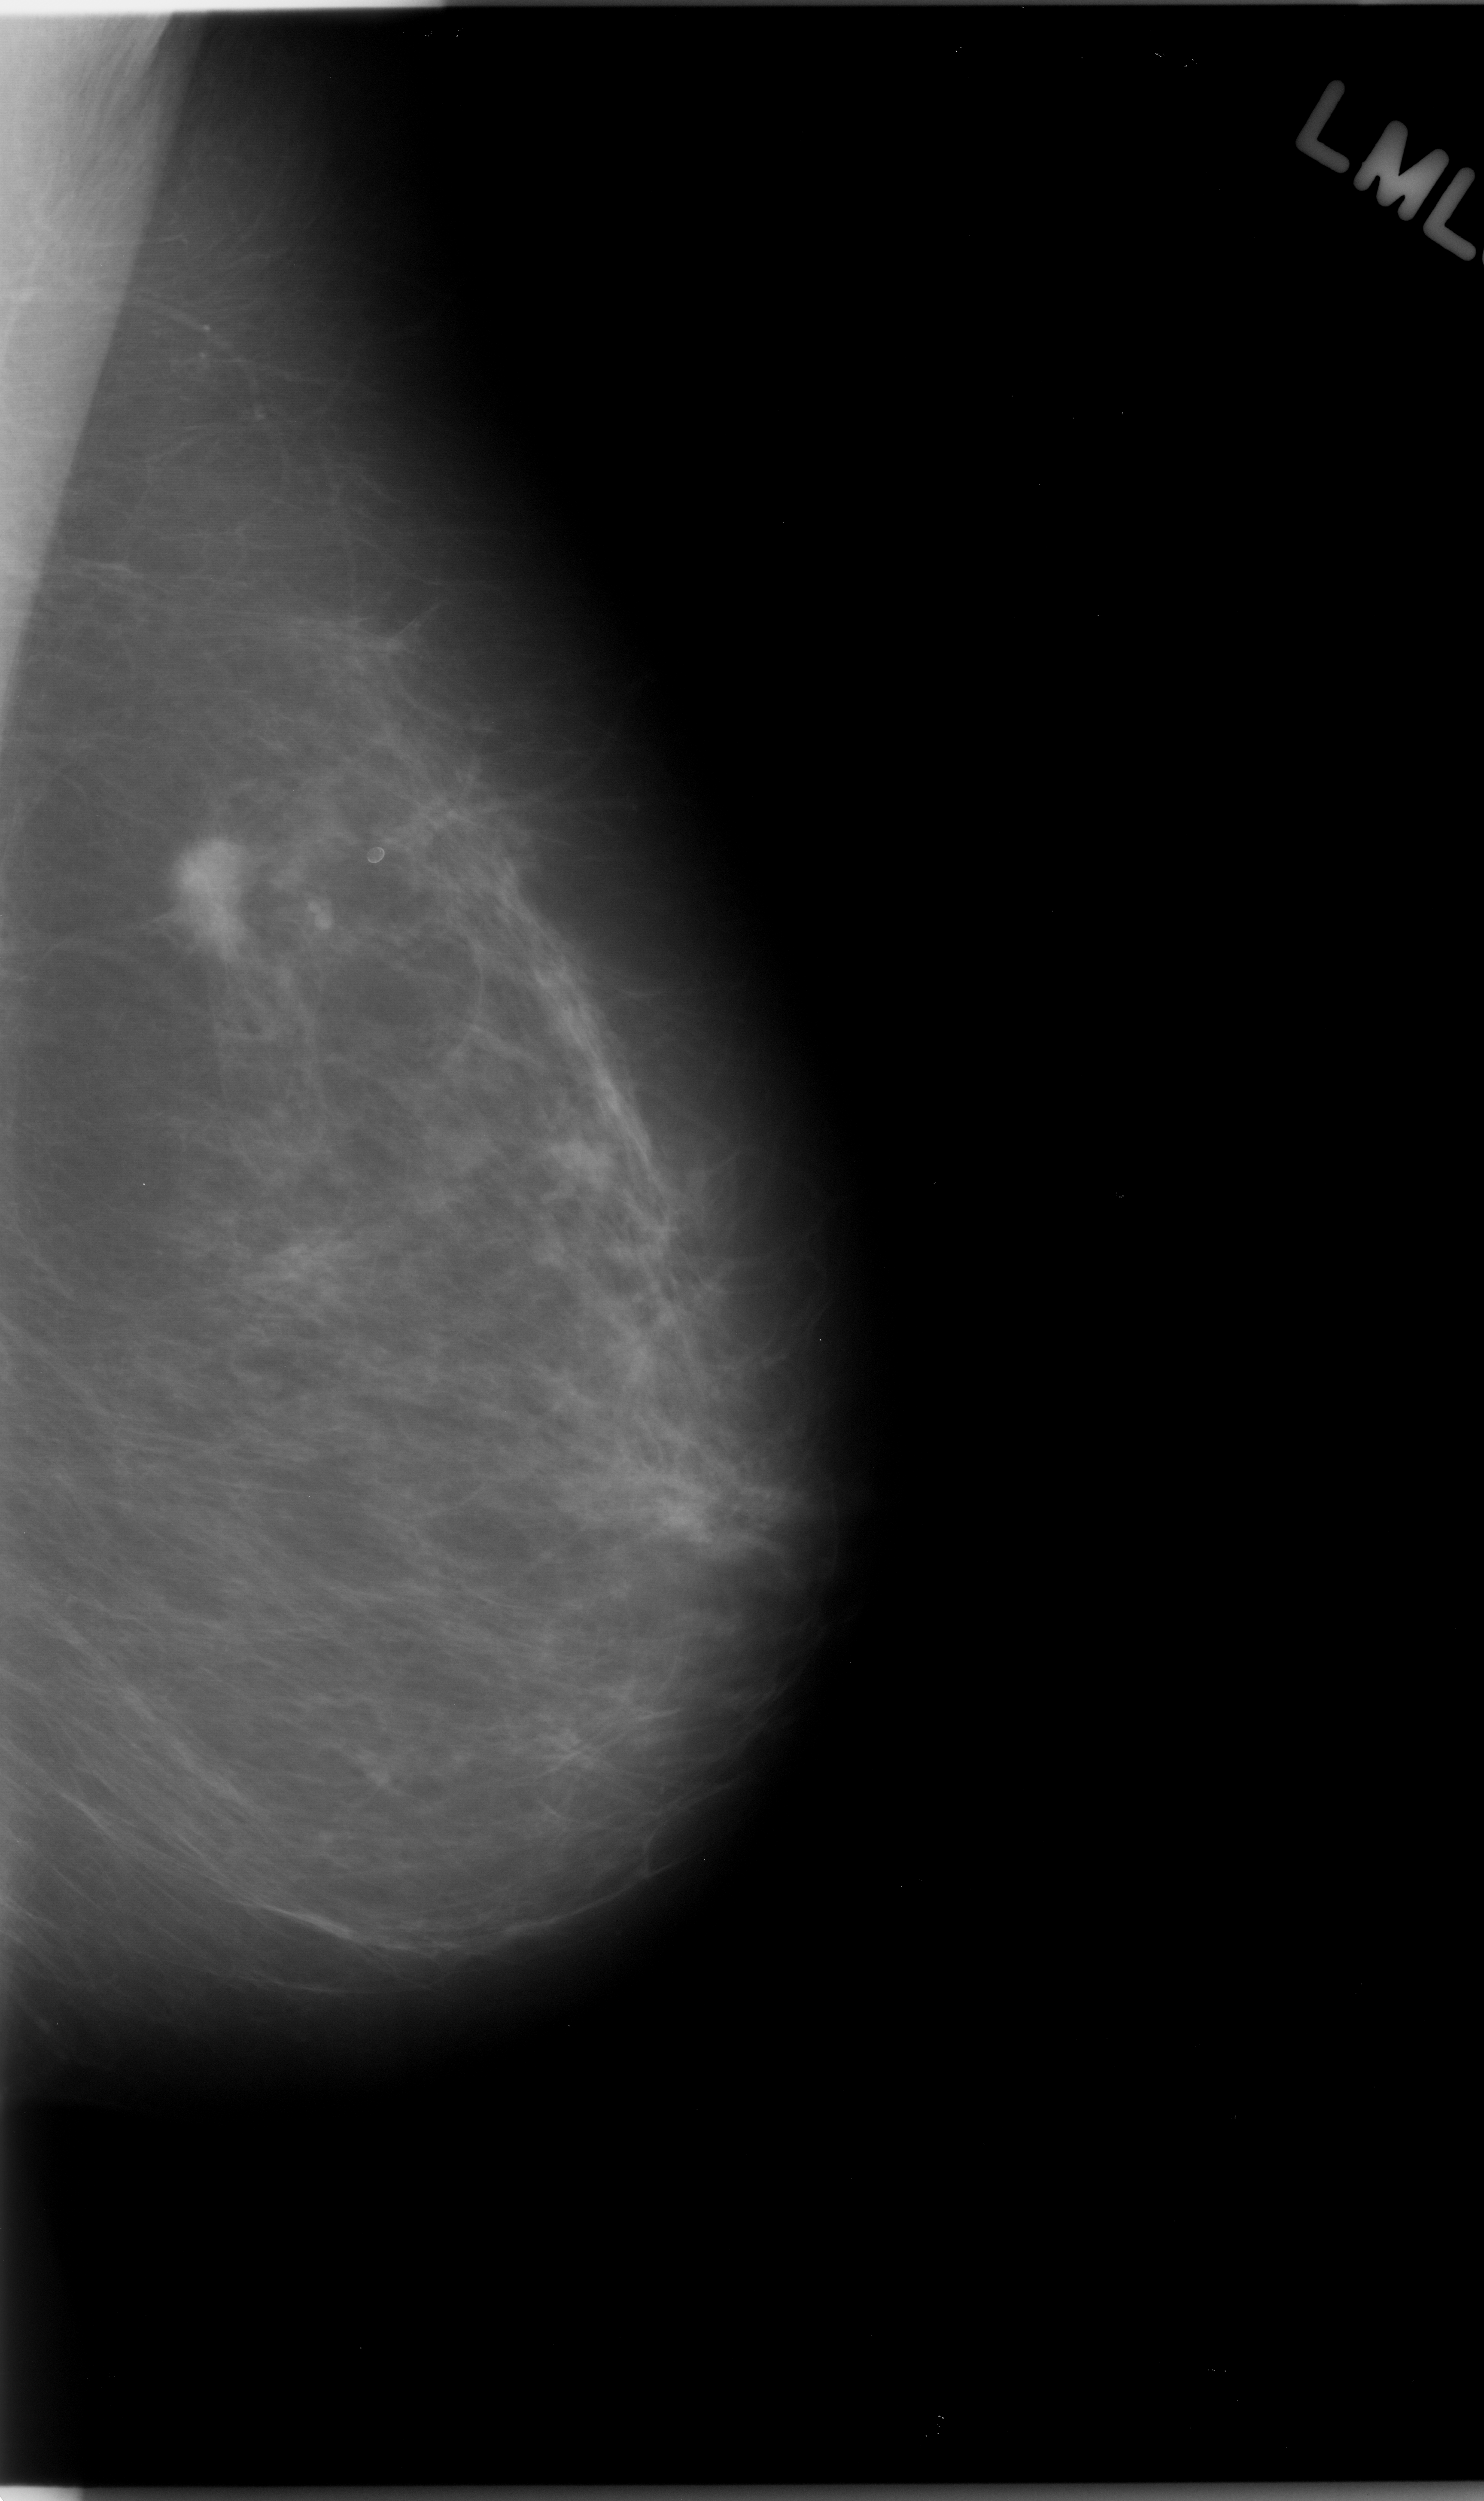
Scanned film-screen mammogram, left breast, MLO view, breast composition: almost entirely fatty (BI-RADS density category 1 of 4).
Abnormality record for this image: mass, shape lobulated, margins spiculated; BI-RADS assessment category 5; pathology (as recorded): malignant.